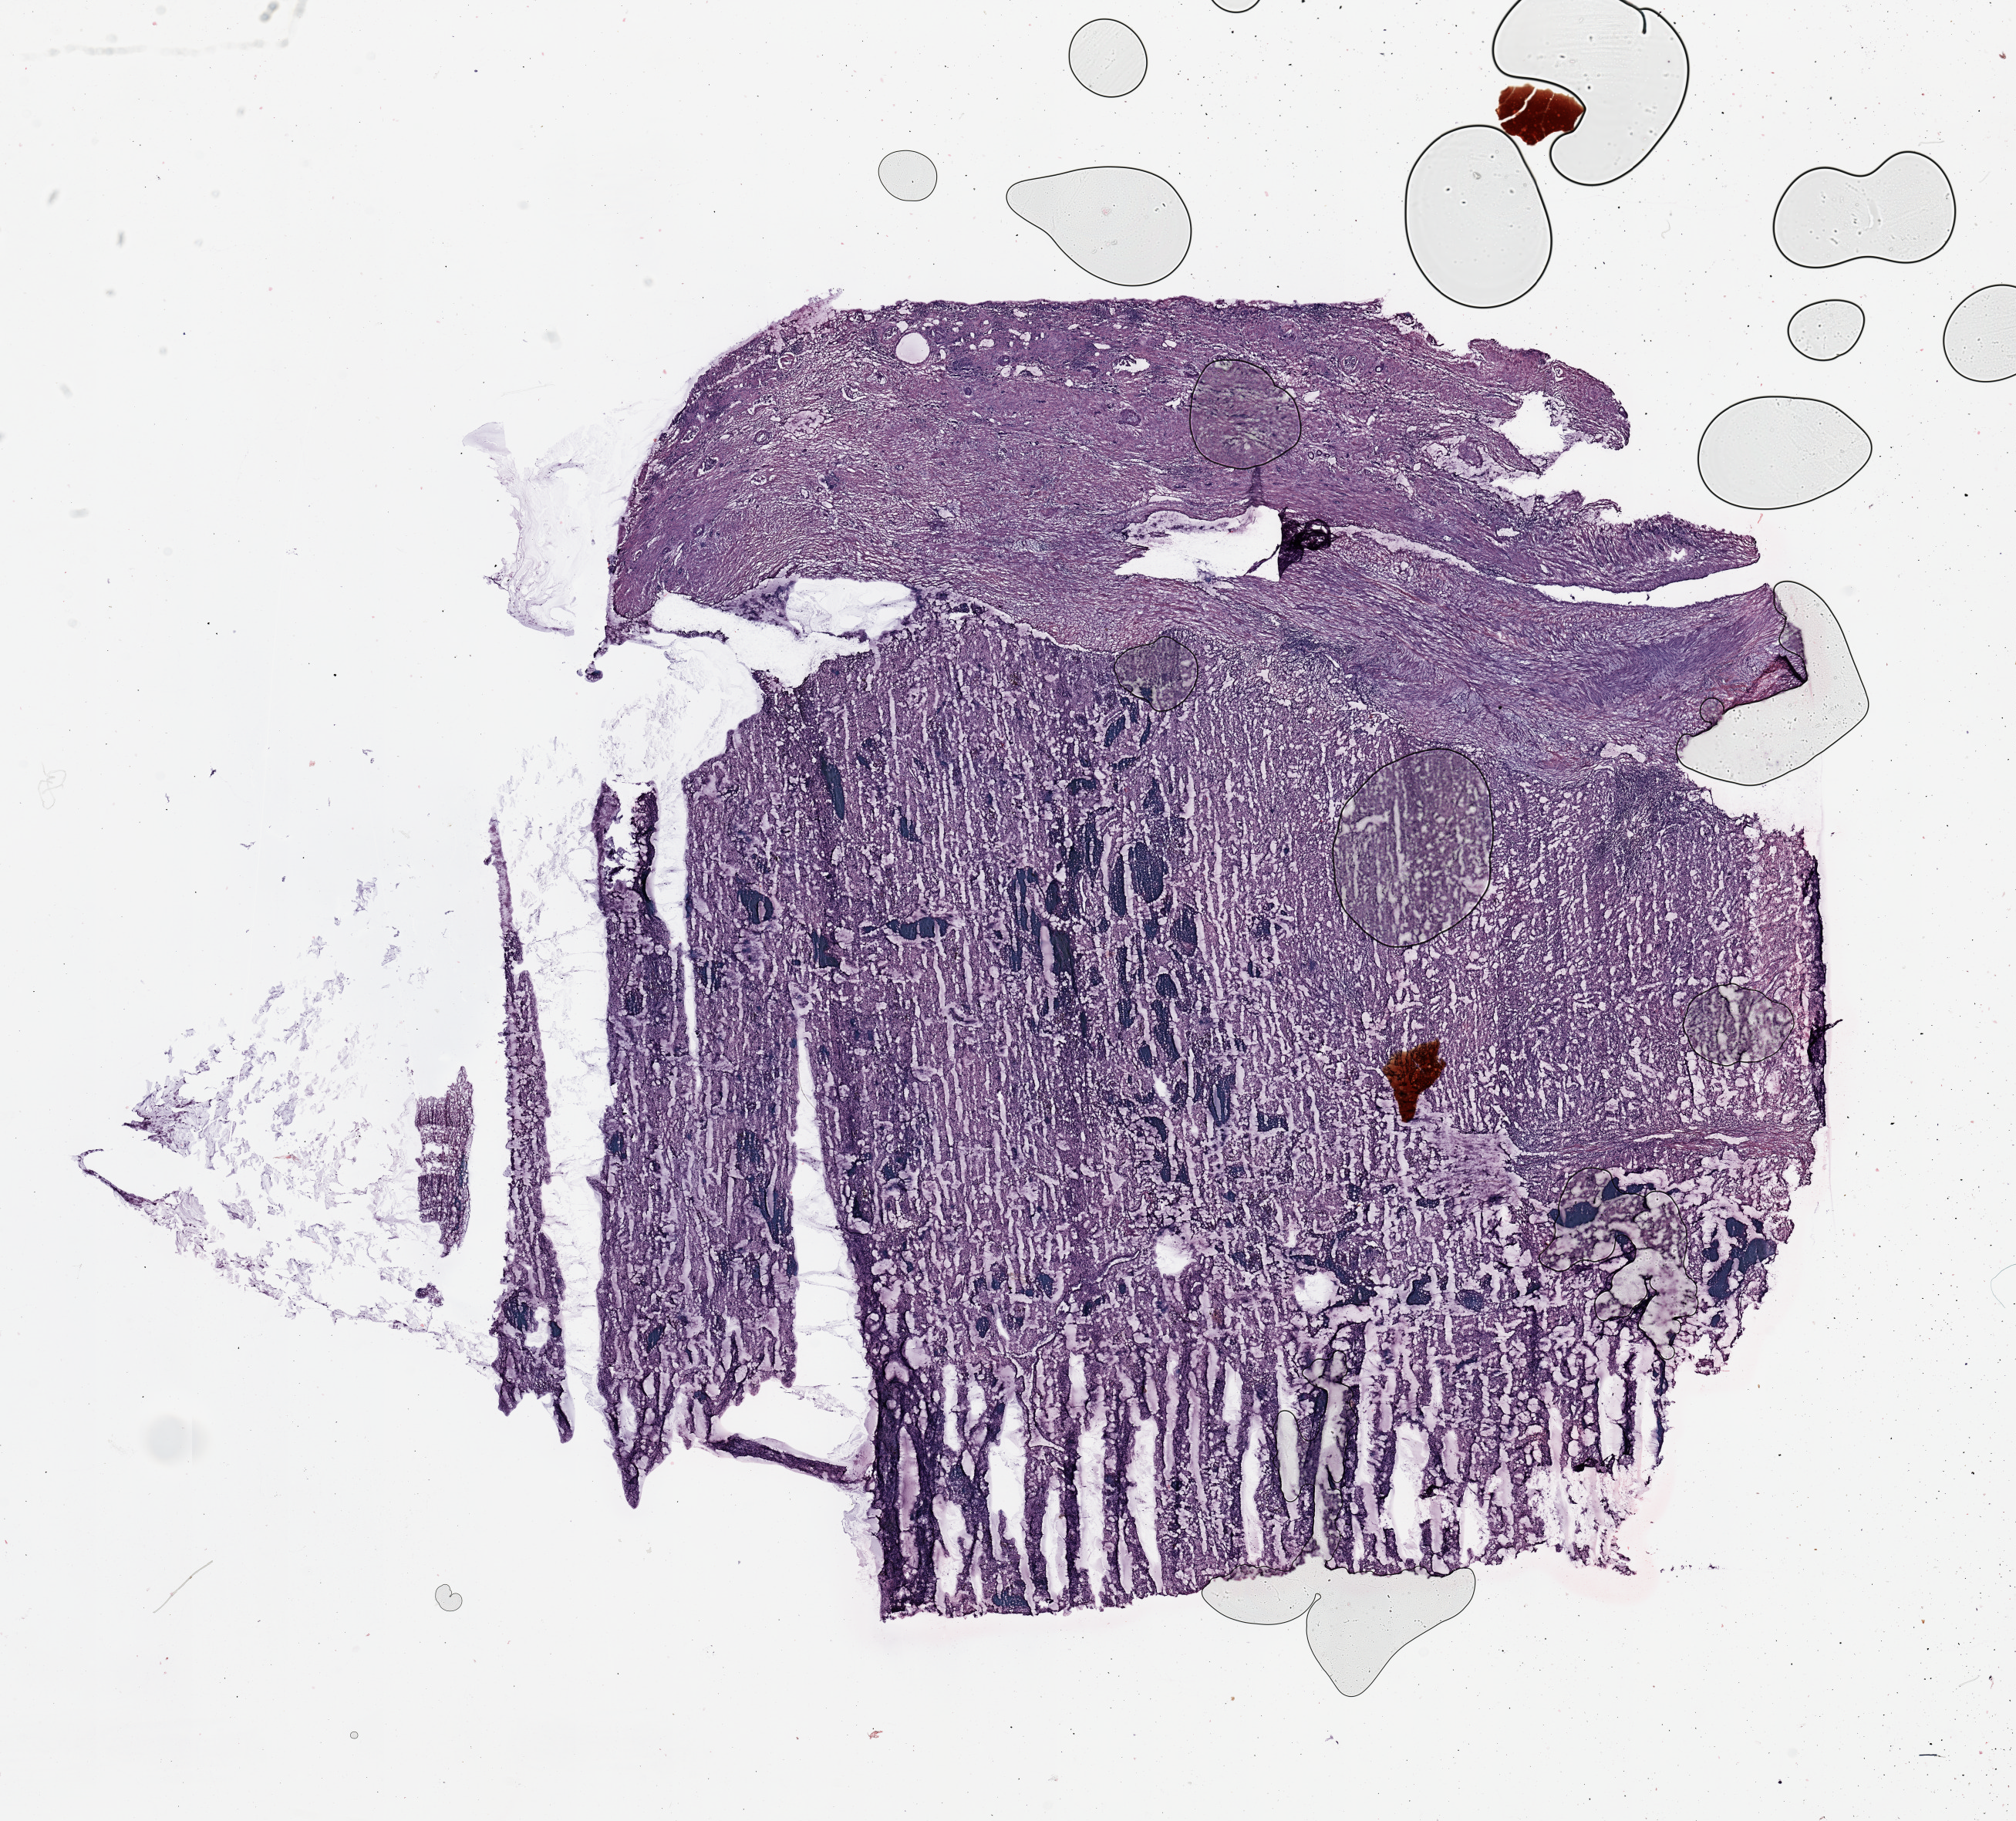
Whole-slide histology image, H&E — shown as a low-resolution overview of the whole scanned area (about 20.7 x 18.7 mm), tumour tissue sample, sampled site: kidney. Female, 57 y/o. Histologic grade: G2 (moderately differentiated). Composition of this section per pathologist review: tumour nuclei 90%, necrosis 5%.
• diagnosis: Renal cell carcinoma, NOS
• AJCC pathologic stage: I
• primary tumour site (as recorded): upper pole